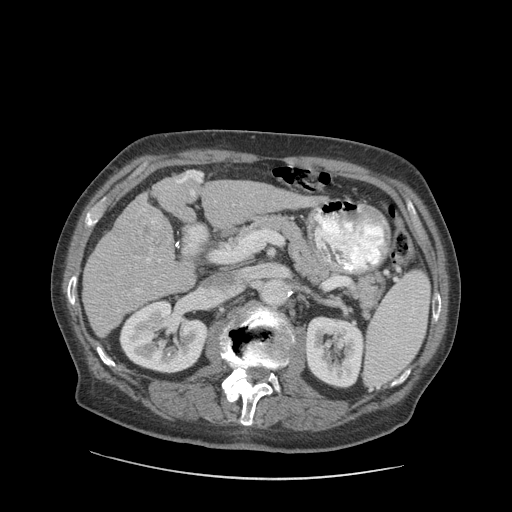
Contrast-enhanced abdominal CT (liver protocol), one axial slice; slice 43 of 89 in the series (ordered by position); soft-tissue window (W 400 / L 40 HU); 2.5 mm slice thickness; 512 × 512 image matrix, field of view 420 × 420 mm. Case-level facts recorded for this patient, not image findings: diagnosis: hepatocellular carcinoma (patient treated with transarterial chemoembolisation; whether this scan precedes or follows treatment is not stated here); TNM stage (as recorded): Stage-I; Child-Pugh class: A; tumour differentiation: moderately differentiated; tumour nodularity: uninodular.
Outlined on this slice (semi-automatic segmentation, software-assisted and operator-edited):
- liver parenchyma outside the tumour (the mass and vessels are separate outlines, so this box may not span the whole liver): bounding box [x1, y1, x2, y2] px = [82, 170, 314, 336]
- mass: [122, 206, 173, 261]
- liver vessels: [117, 171, 308, 312]